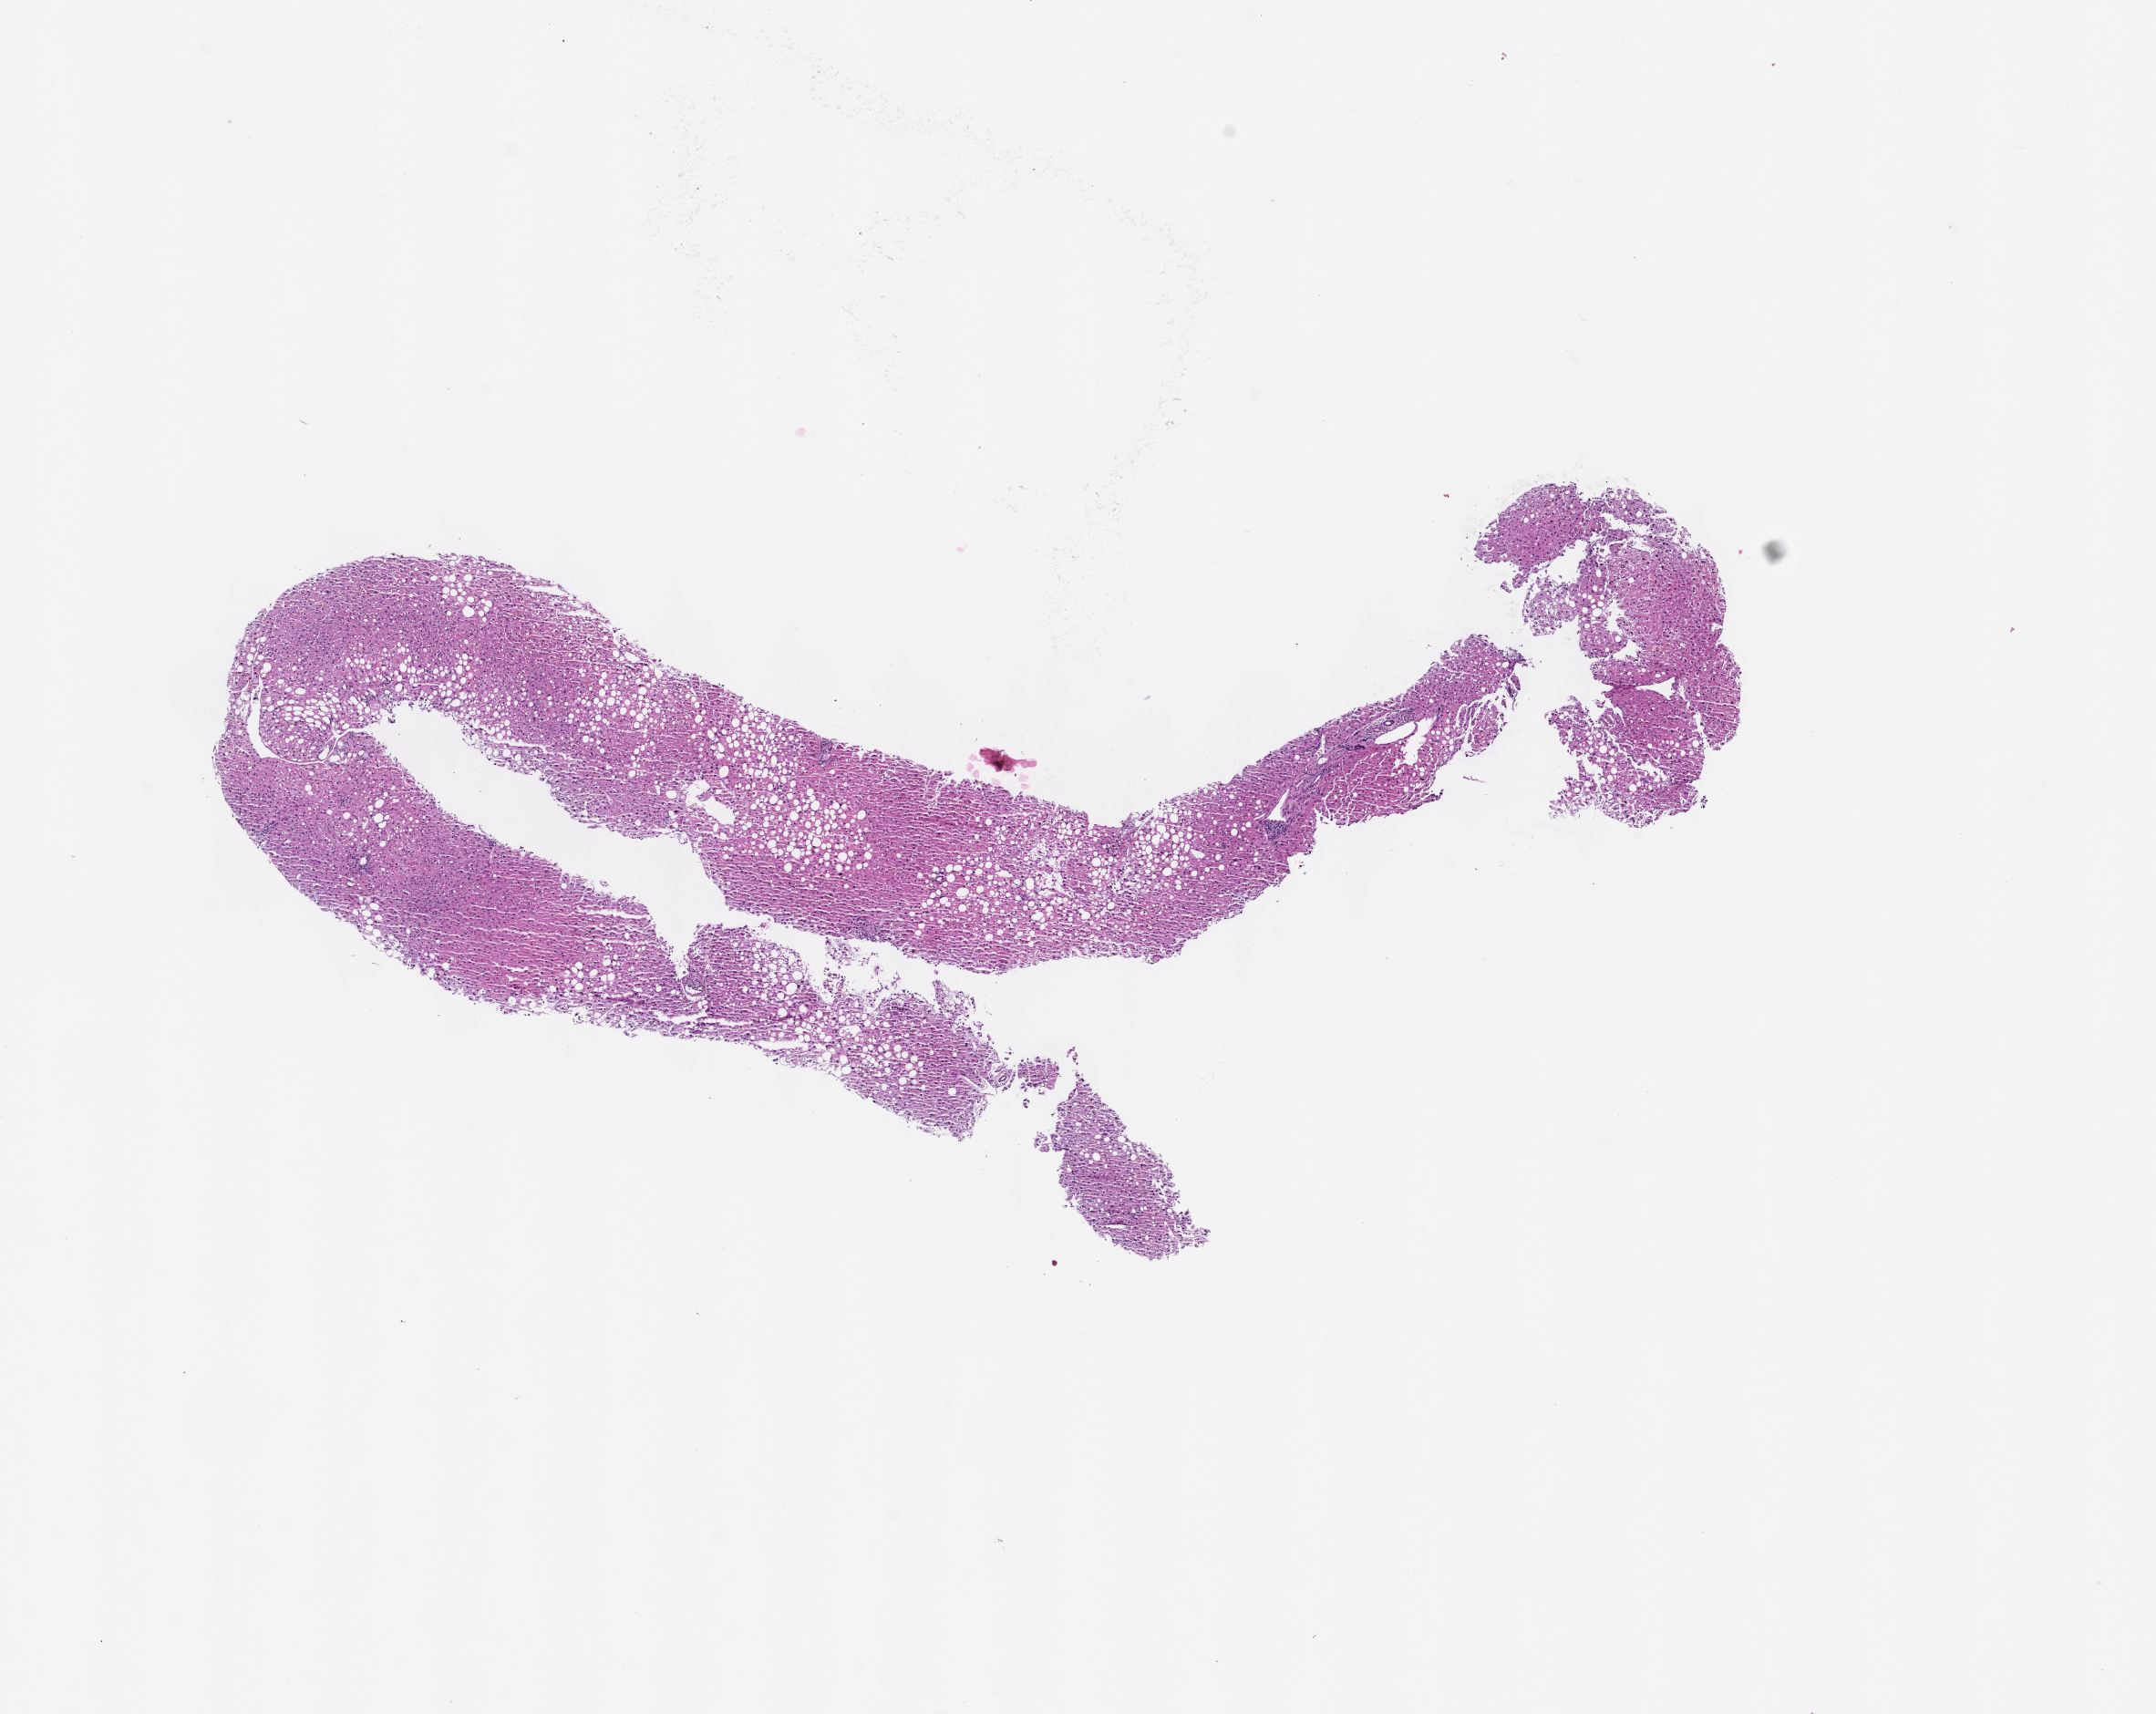
Digitized H&E-stained section — shown as a low-resolution overview of the whole scanned area (about 9.5 x 7.6 mm), formalin-fixed paraffin-embedded section, collected at baseline (before treatment). Male patient.
This section: metastatic tumor tissue. Patient diagnosis (primary): Melanoma.